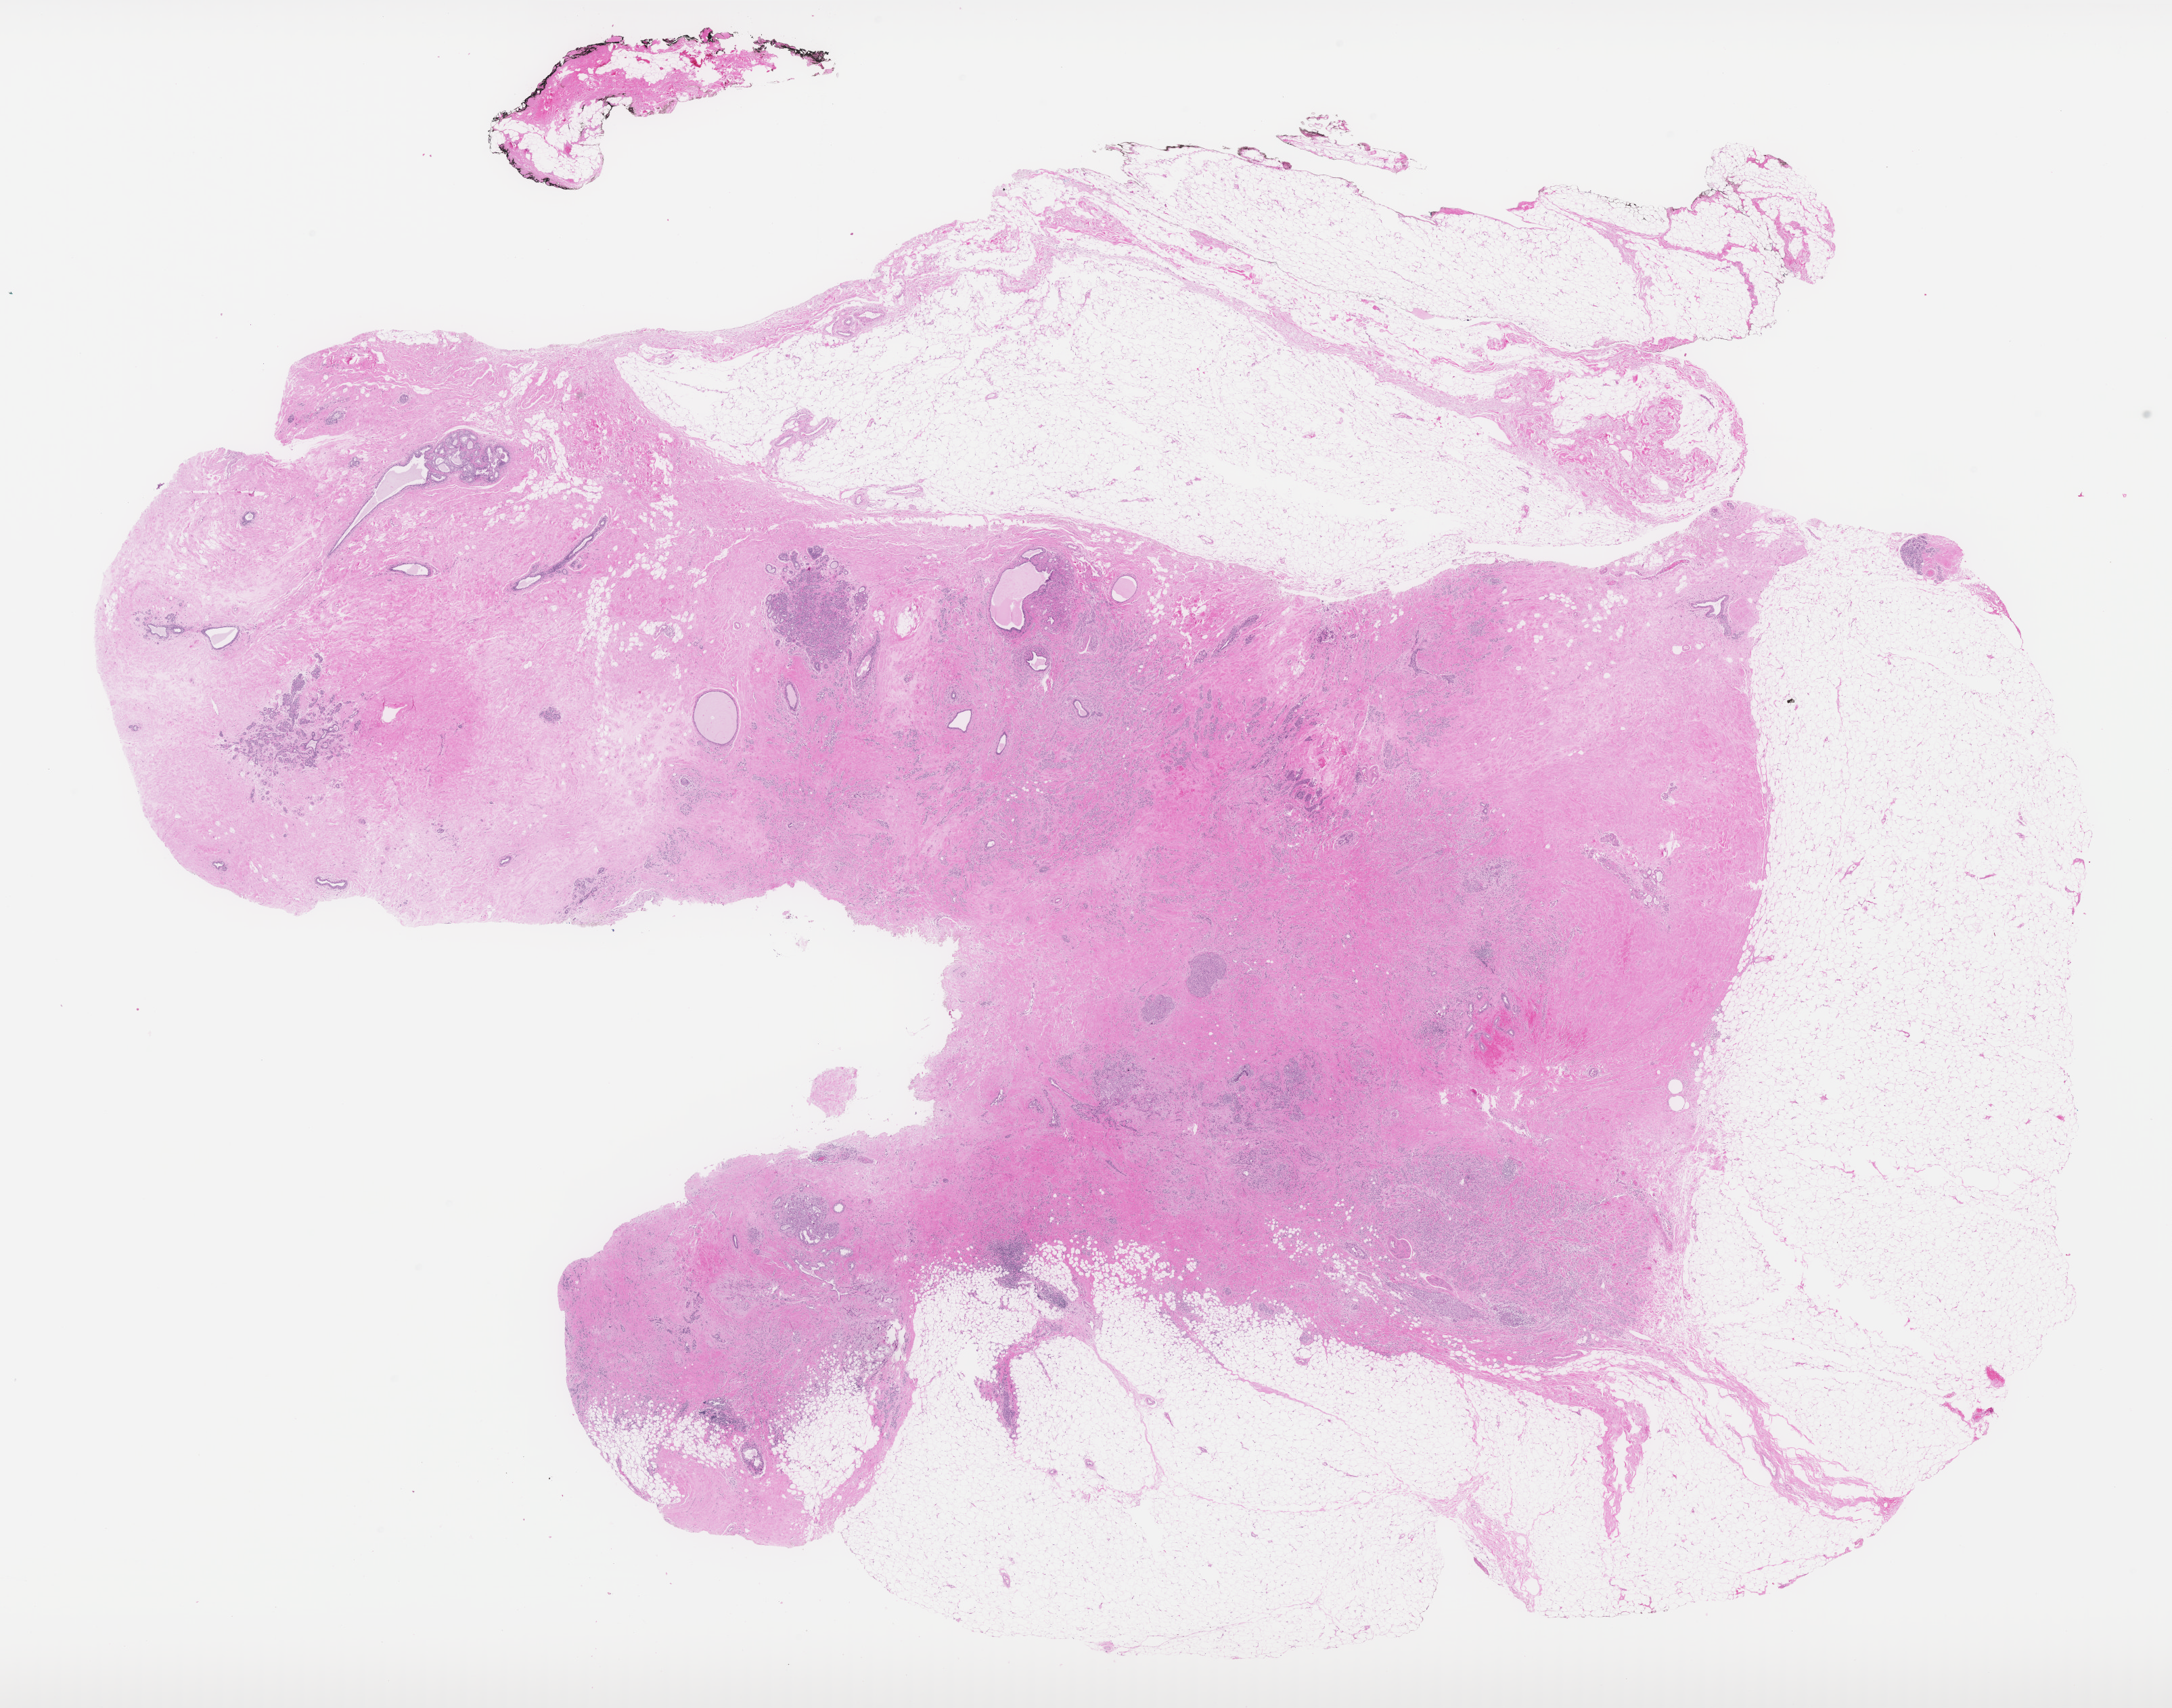
Whole-slide histology image, H&E — shown as a low-resolution overview of the whole scanned area (about 25.7 x 20.2 mm, from a 40x scan); formalin-fixed paraffin-embedded (FFPE) diagnostic section; sample: primary tumour, breast. Female, age 61 years at initial diagnosis.
* AJCC pathologic stage: IIA
* histologic diagnosis: Lobular carcinoma, NOS
* laterality: left